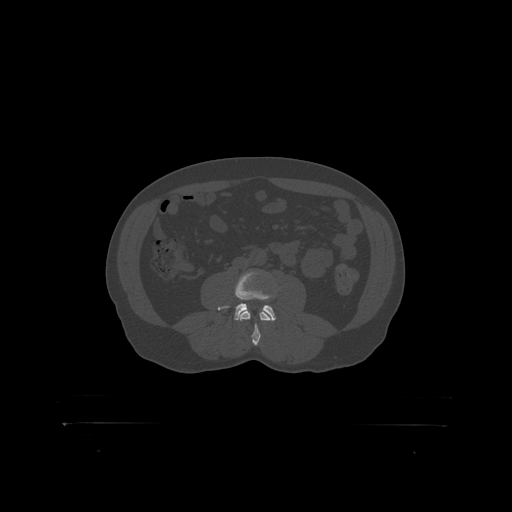
CT including the spine, one axial slice. Slice 250 of 399 in the series (ordered by position). Reconstruction kernel STANDARD. 120 kVp. Bone window (W 1800 / L 400 HU). 1.25 mm slice thickness. 512 × 512 image matrix, field of view 650 × 650 mm. Patient: male, 46 years. Case-level facts recorded for this patient, not image findings: primary cancer: skin.
Outlined on this slice (semi-automatically segmented with operator editing):
- L3 vertebra: bounding box (x1, y1, x2, y2) in pixels: (240, 310, 269, 319)
- L4 vertebra: (221, 272, 275, 317)